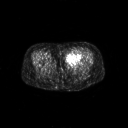
FDG PET of an extremity soft-tissue mass (from a PET/CT study), one axial slice. Slice 24 of 267 in the series (ordered by position). 3.27 mm slice thickness. 128 × 128 image matrix, field of view 700 × 700 mm. Female patient, age 47 years. From the clinical record (not read from this slice): histological type: myxofibrosarcoma; grade: intermediate; site of the primary tumour: left thigh.
Structures marked on this image (expert contour drawn on MRI and transferred to this co-registered scan by the dataset authors):
- gross tumour volume including surrounding oedema: bounding box [x1, y1, x2, y2] px = [65, 51, 82, 65]
- gross tumour volume (mass): [66, 51, 82, 64]